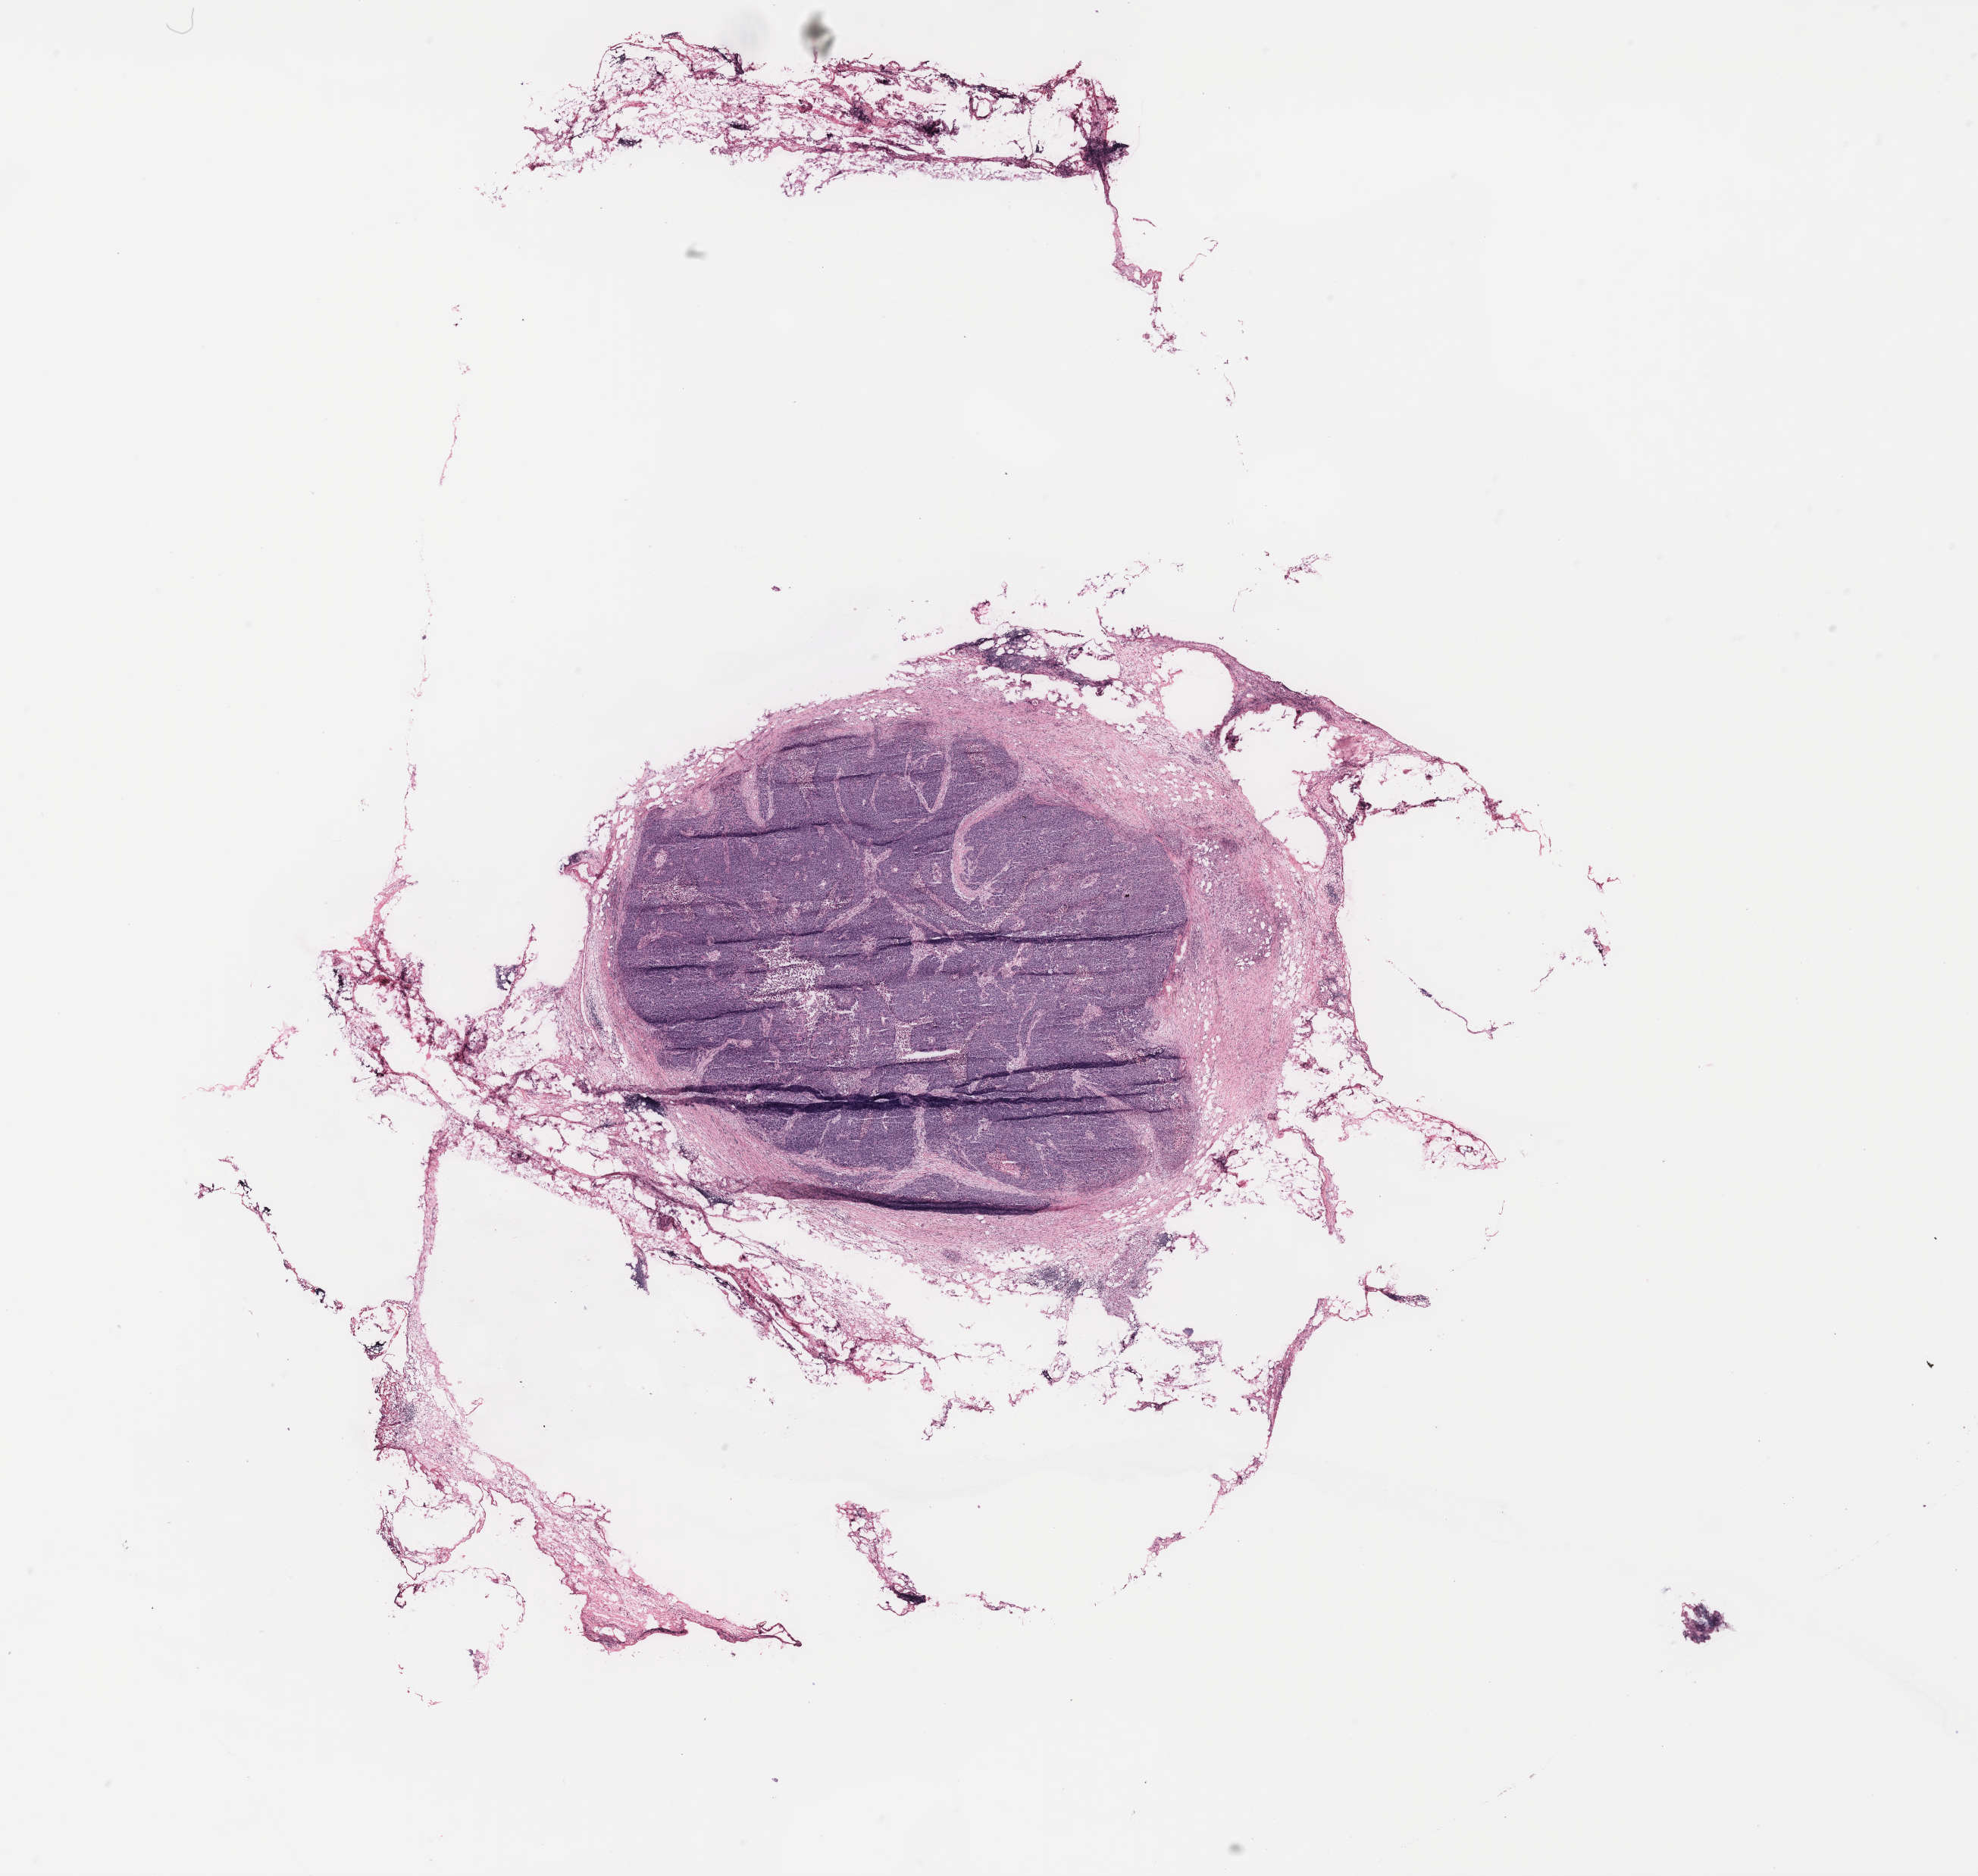
H&E-stained whole-slide image, shown as a low-resolution overview of the whole scanned area (about 20.9 x 19.8 mm); ovary, tissue type not recorded. Patient sex: female.
Patient diagnosis: Serous adenocarcinoma, NOS.